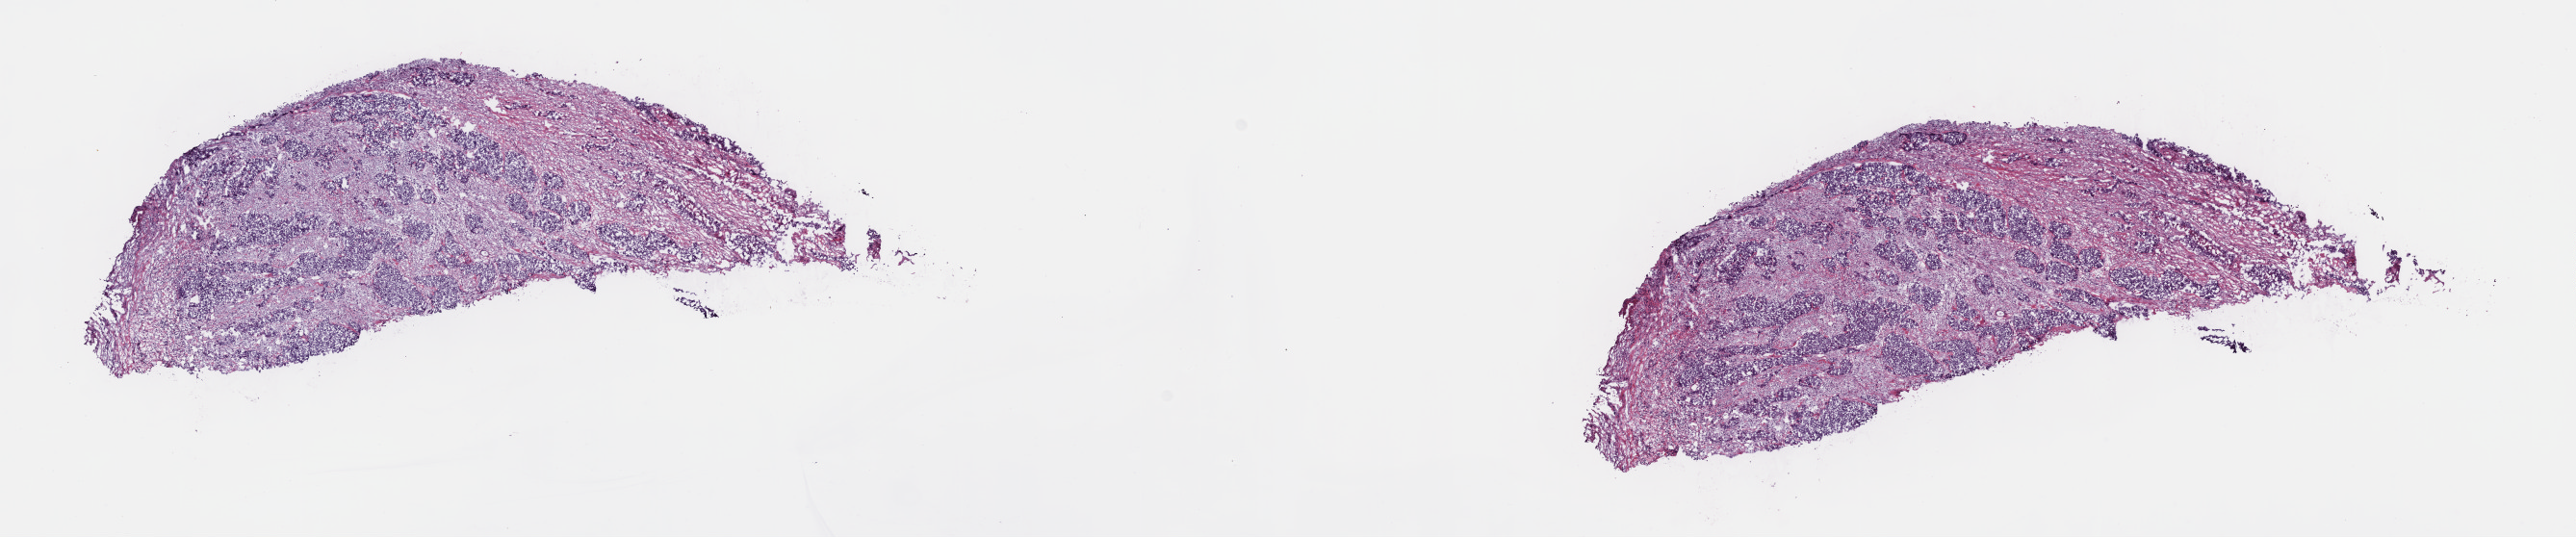
Whole-slide histology image, H&E, whole scanned area (about 21.6 x 4.5 mm, from a 40x scan) shown as a low-resolution overview, frozen section, sample: primary tumour, bladder. Patient: male, age at initial diagnosis 65 years. Histologic grade: high grade. Composition of this section per pathologist review: tumour cells 70%, tumour nuclei 70%, normal cells 0%, stromal cells 30%, necrosis 0%. Inflammatory infiltration, as recorded: lymphocyte infiltration 3%, monocyte infiltration 1%, neutrophil infiltration 5%.
- AJCC pathologic stage: III
- histologic diagnosis: Transitional cell carcinoma (lateral wall of bladder)
- TNM: T3a N0 M0